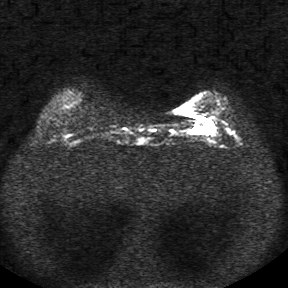
Breast MRI, one axial slice; position 7 of 34 along the scan axis; diffusion-weighted series; image 2 of 4 stored at this slice position (different b-values; order by instance number); 1.5 T; 288 × 288 image matrix, field of view 340 × 340 mm. Female patient.
Structures marked on this image (manually delineated by an expert):
- tumour on diffusion-weighted imaging: bounding box [x1, y1, x2, y2] px = [192, 122, 214, 134]